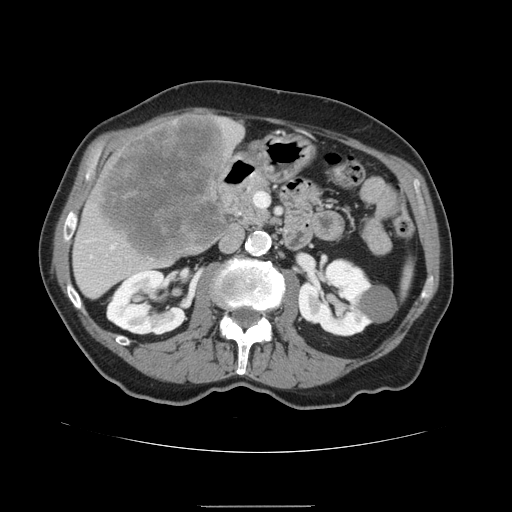
Contrast-enhanced abdominal CT, one axial slice; 120 kVp; soft-tissue window (W 400 / L 40 HU); 512 × 512 image matrix, field of view 386 × 386 mm. Male patient, age 74 years. Case-level facts recorded for this patient, not image findings: diagnosis: colorectal cancer liver metastases, imaged before liver resection.
Outlined on this slice (expert manual segmentation):
- liver: bounding box <72,114,245,299> (left, top, right, bottom; pixels)
- liver metastasis: <101,117,228,260>